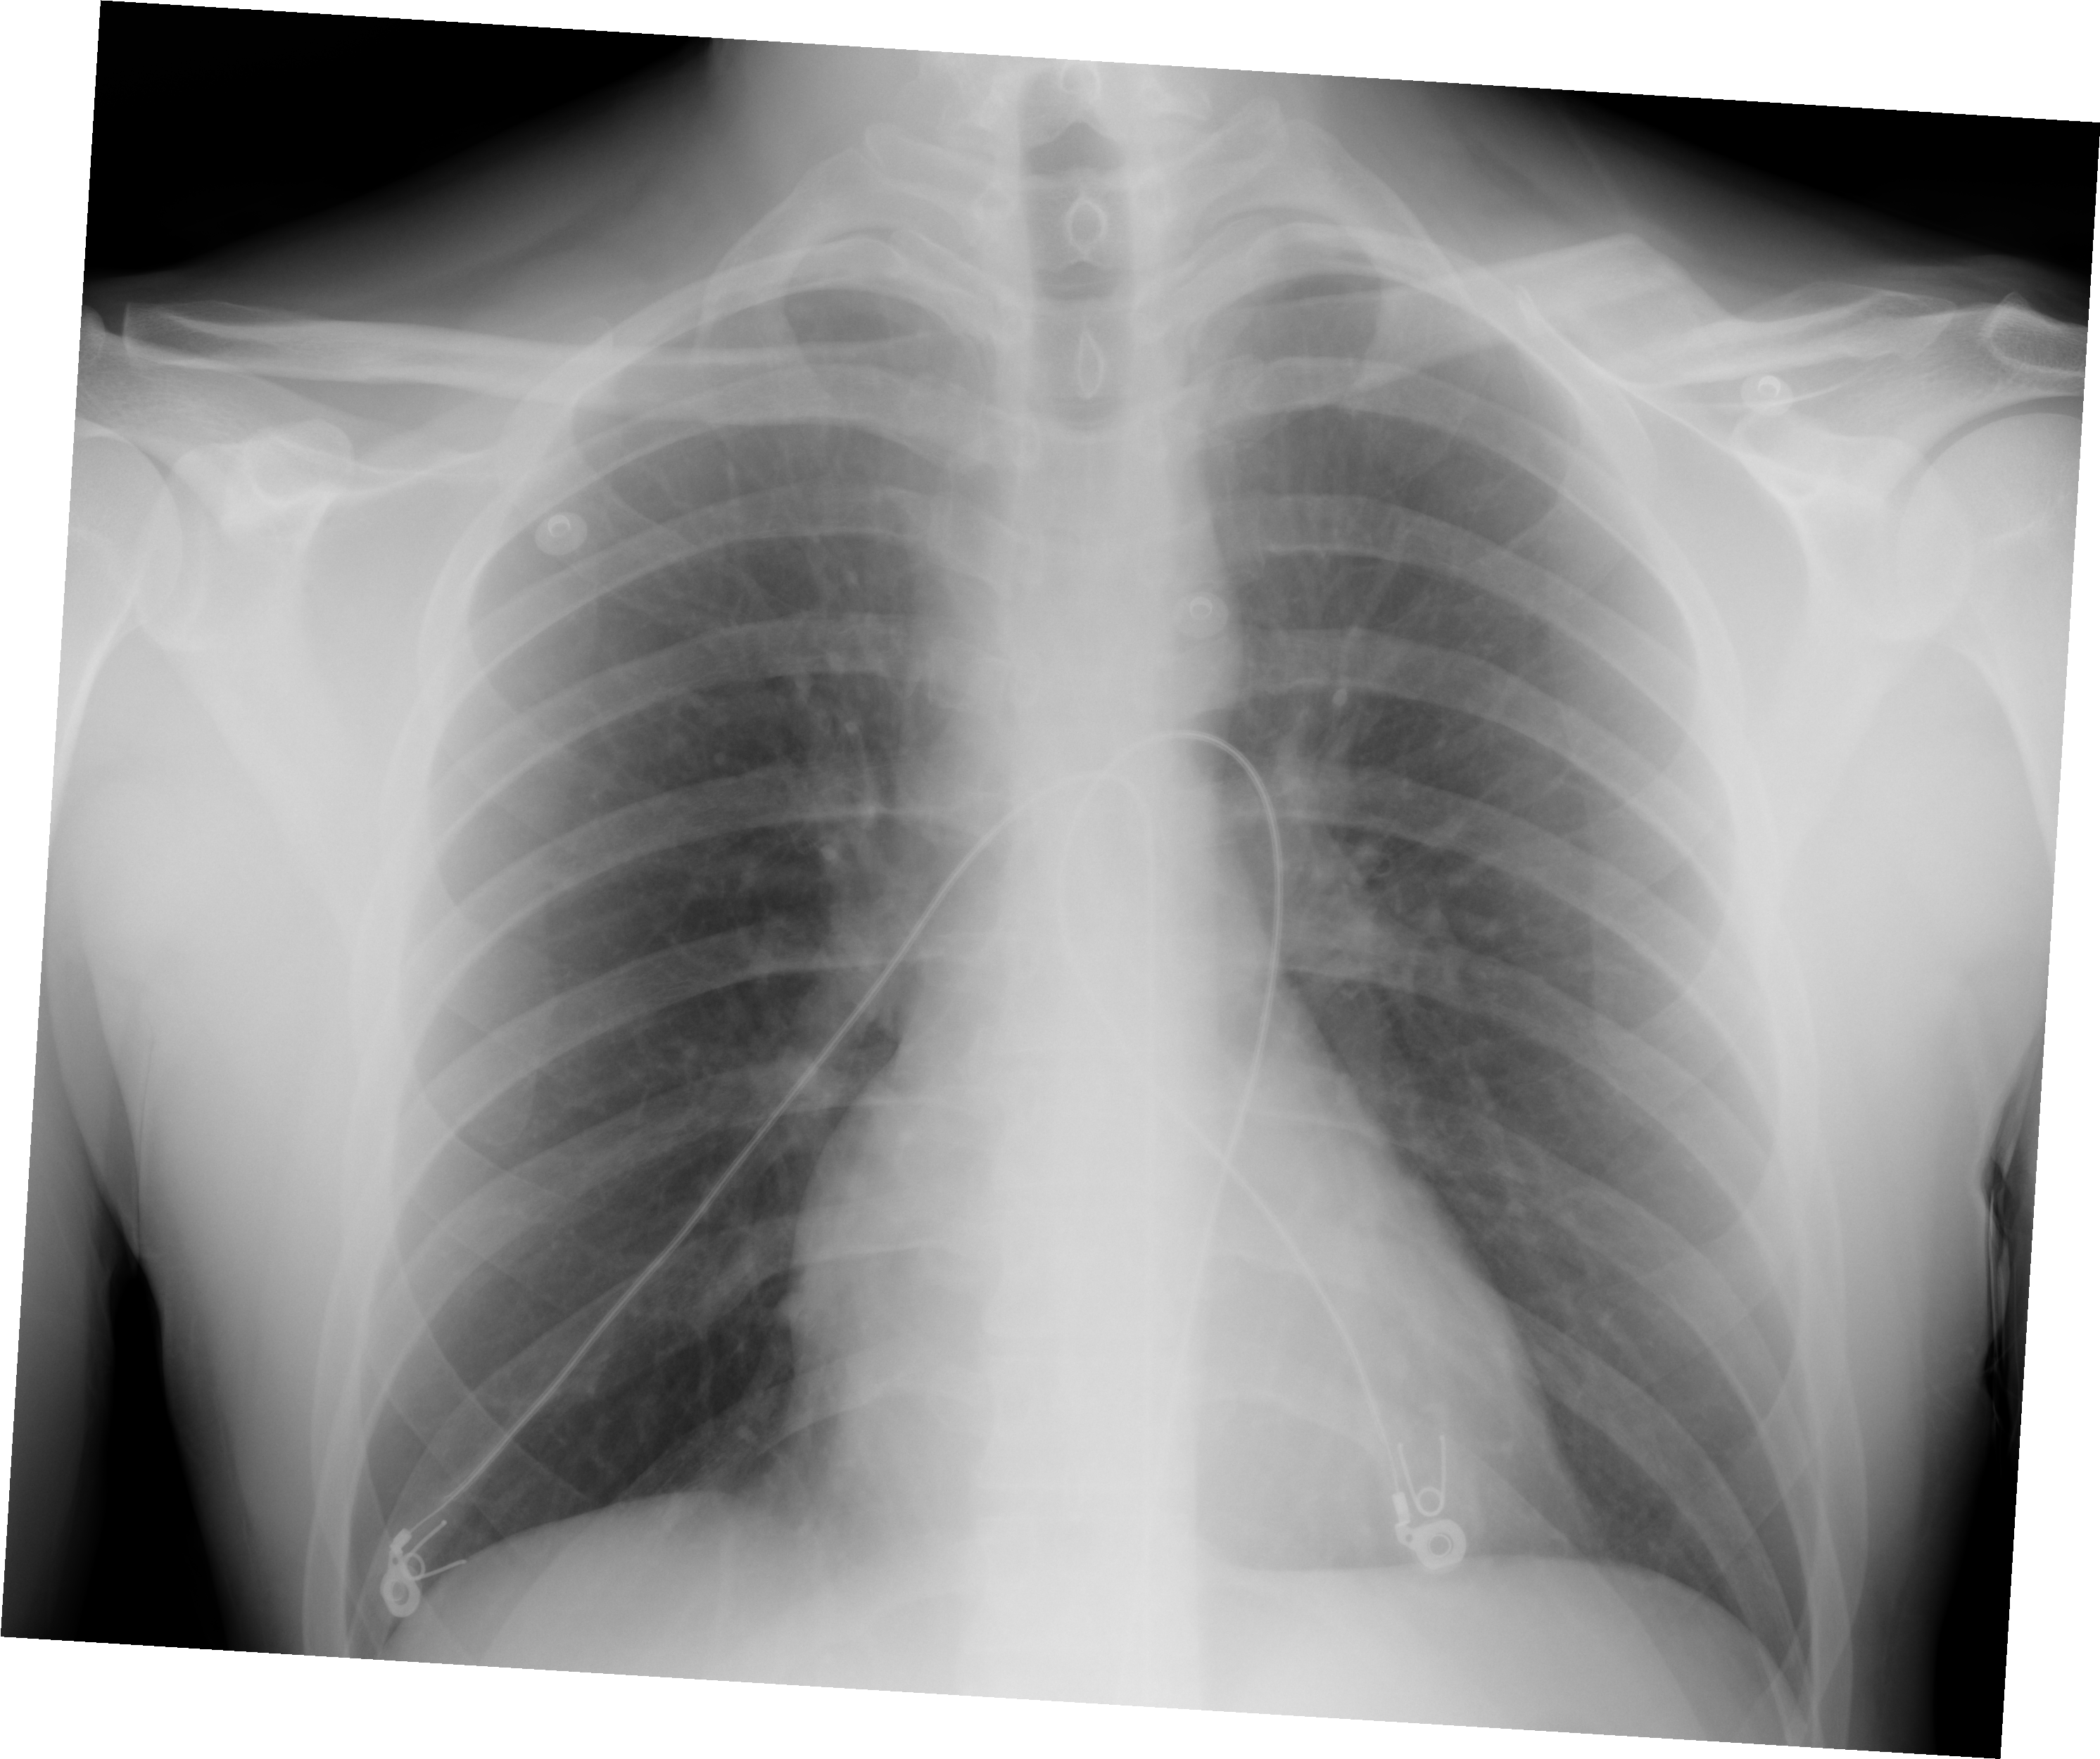
Chest X-ray (portable), AP projection. Male patient, age 26 years; imaged 0 days after the COVID-19 diagnosis.
Radiologist's key findings for this exam: he lungs are clear without focal airspace opacification.